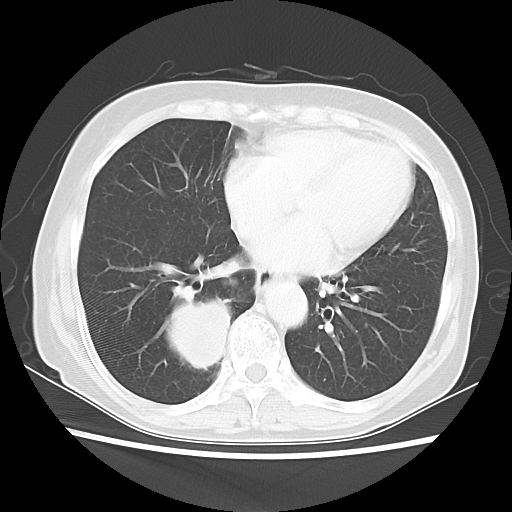
Chest CT, one axial slice; slice 21 of 56 in the series (ordered by position); reconstruction kernel LUNG; lung window (W 1500 / L -600 HU); 5 mm slice thickness; 512 × 512 image matrix. Female patient, age 66 years. Case-level facts recorded for this patient, not image findings: clinical TNM (as recorded): T2 N3 M0; histopathological grade: G3.
Annotated regions visible in this slice (bounding box drawn by a radiologist):
- lung tumour (recorded histology: small cell carcinoma): bounding box <164,290,239,385> (left, top, right, bottom; pixels)